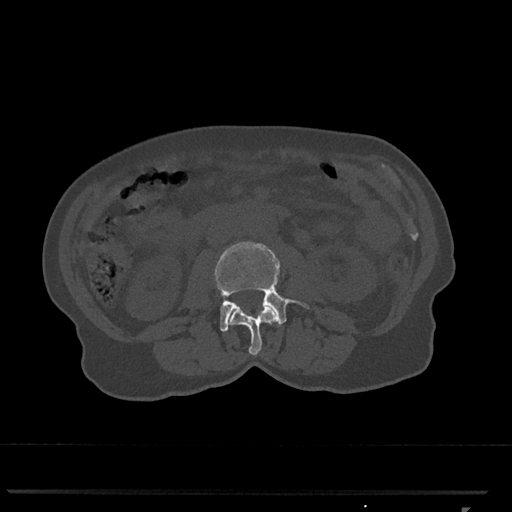
CT including the spine, one axial slice. Position 298 of 793 along the scan axis. Bone window (W 1800 / L 400 HU). 0.5 mm slice thickness. 512 × 512 image matrix. Patient: female, 62 years. From the clinical record (not read from this slice): primary cancer: renal.
Annotated regions visible in this slice (semi-automatically segmented with operator editing):
- L2 vertebra: bounding box [x1, y1, x2, y2] px = [228, 306, 278, 355]
- L3 vertebra: [214, 242, 309, 332]